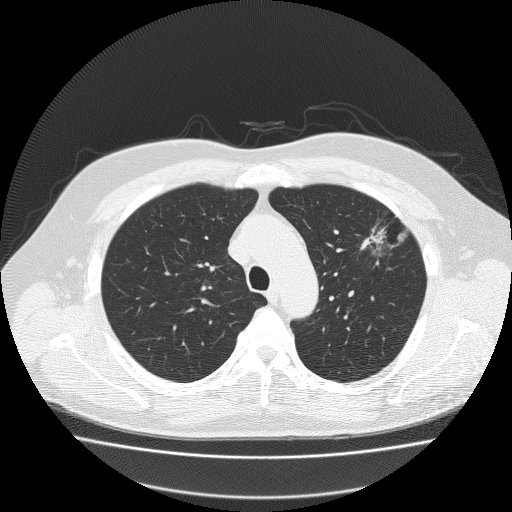
Chest CT (low-dose screening protocol), one axial image, baseline annual screen, lung window (W 1500 / L -600 HU), 512 × 512 image matrix. Male participant, aged 62 years at enrolment. Former smoker at enrolment.
Expert-annotated lung lesion, bounding box [x1, y1, x2, y2] px = [353, 207, 421, 264]. The exam's reader record, not a measurement of the box and not confirmed to be the same lesion: non-calcified nodule or mass ≥4 mm, left upper lobe, 18 × 8 mm, spiculated (stellate) margins, soft tissue attenuation. Later outcome: lung cancer diagnosed 49 days after this screen — bronchiolo-alveolar adenocarcinoma, NOS, left upper lobe, well differentiated (G1), stage IA (AJCC 6th edition), 25 mm at pathology.